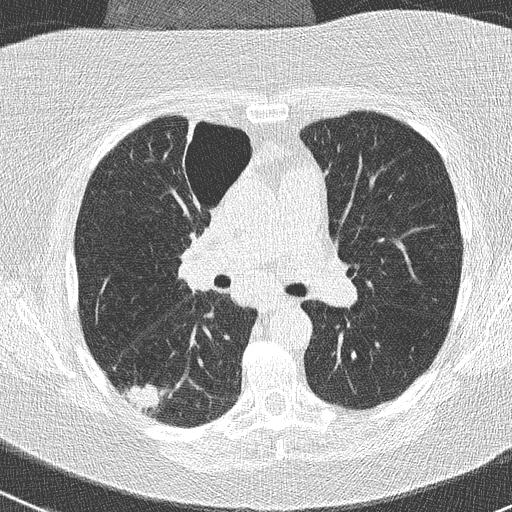
Low-dose screening chest CT, one axial slice; position 156 of 261 along the scan axis; lung window (W 1500 / L -600 HU); 2 mm slice thickness; 512 × 512 image matrix, field of view 310 × 310 mm.
Outlined on this slice (manually delineated by an expert):
- lesion 1 (tumor, lower lobe of right lung): box from (x=125, y=384) to (x=163, y=412) px